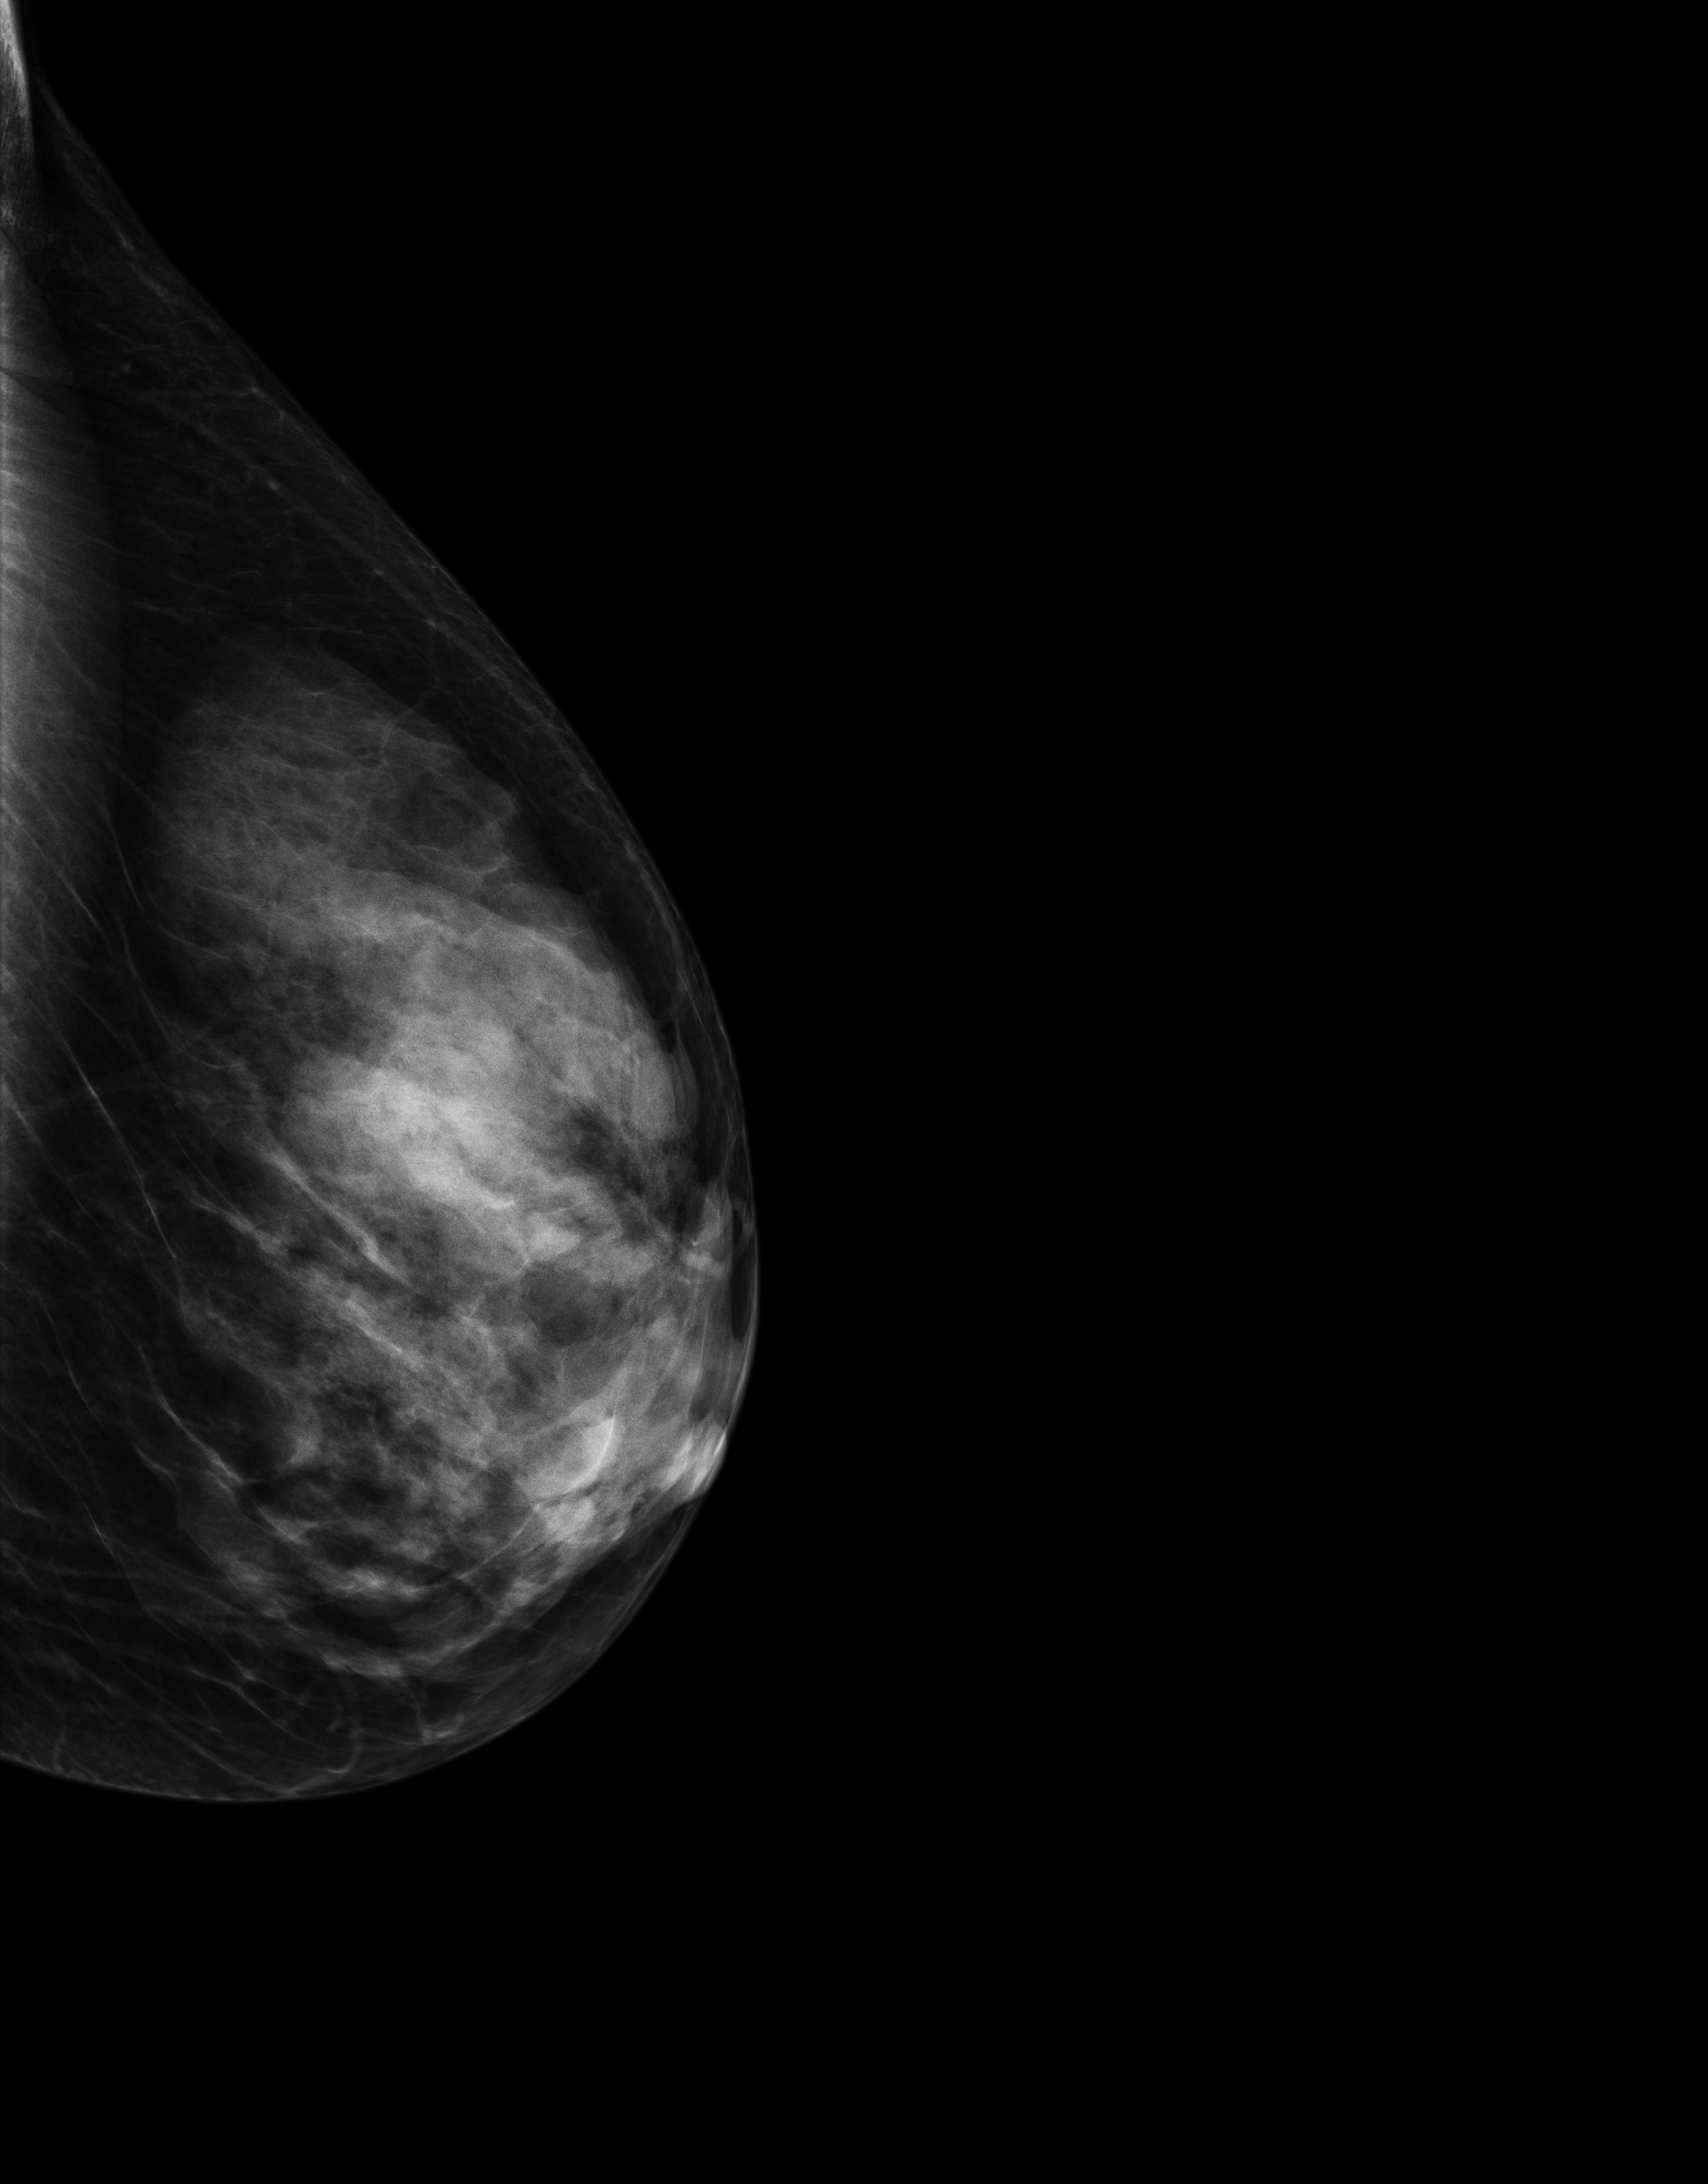
Annual screening mammography examination; system: Senographe Essential ADS_56.21.3. Patient aged 61 years (female).
Image type: full-field digital mammogram. Breast: left. Projection: laterally exaggerated craniocaudal (XCCL) view.